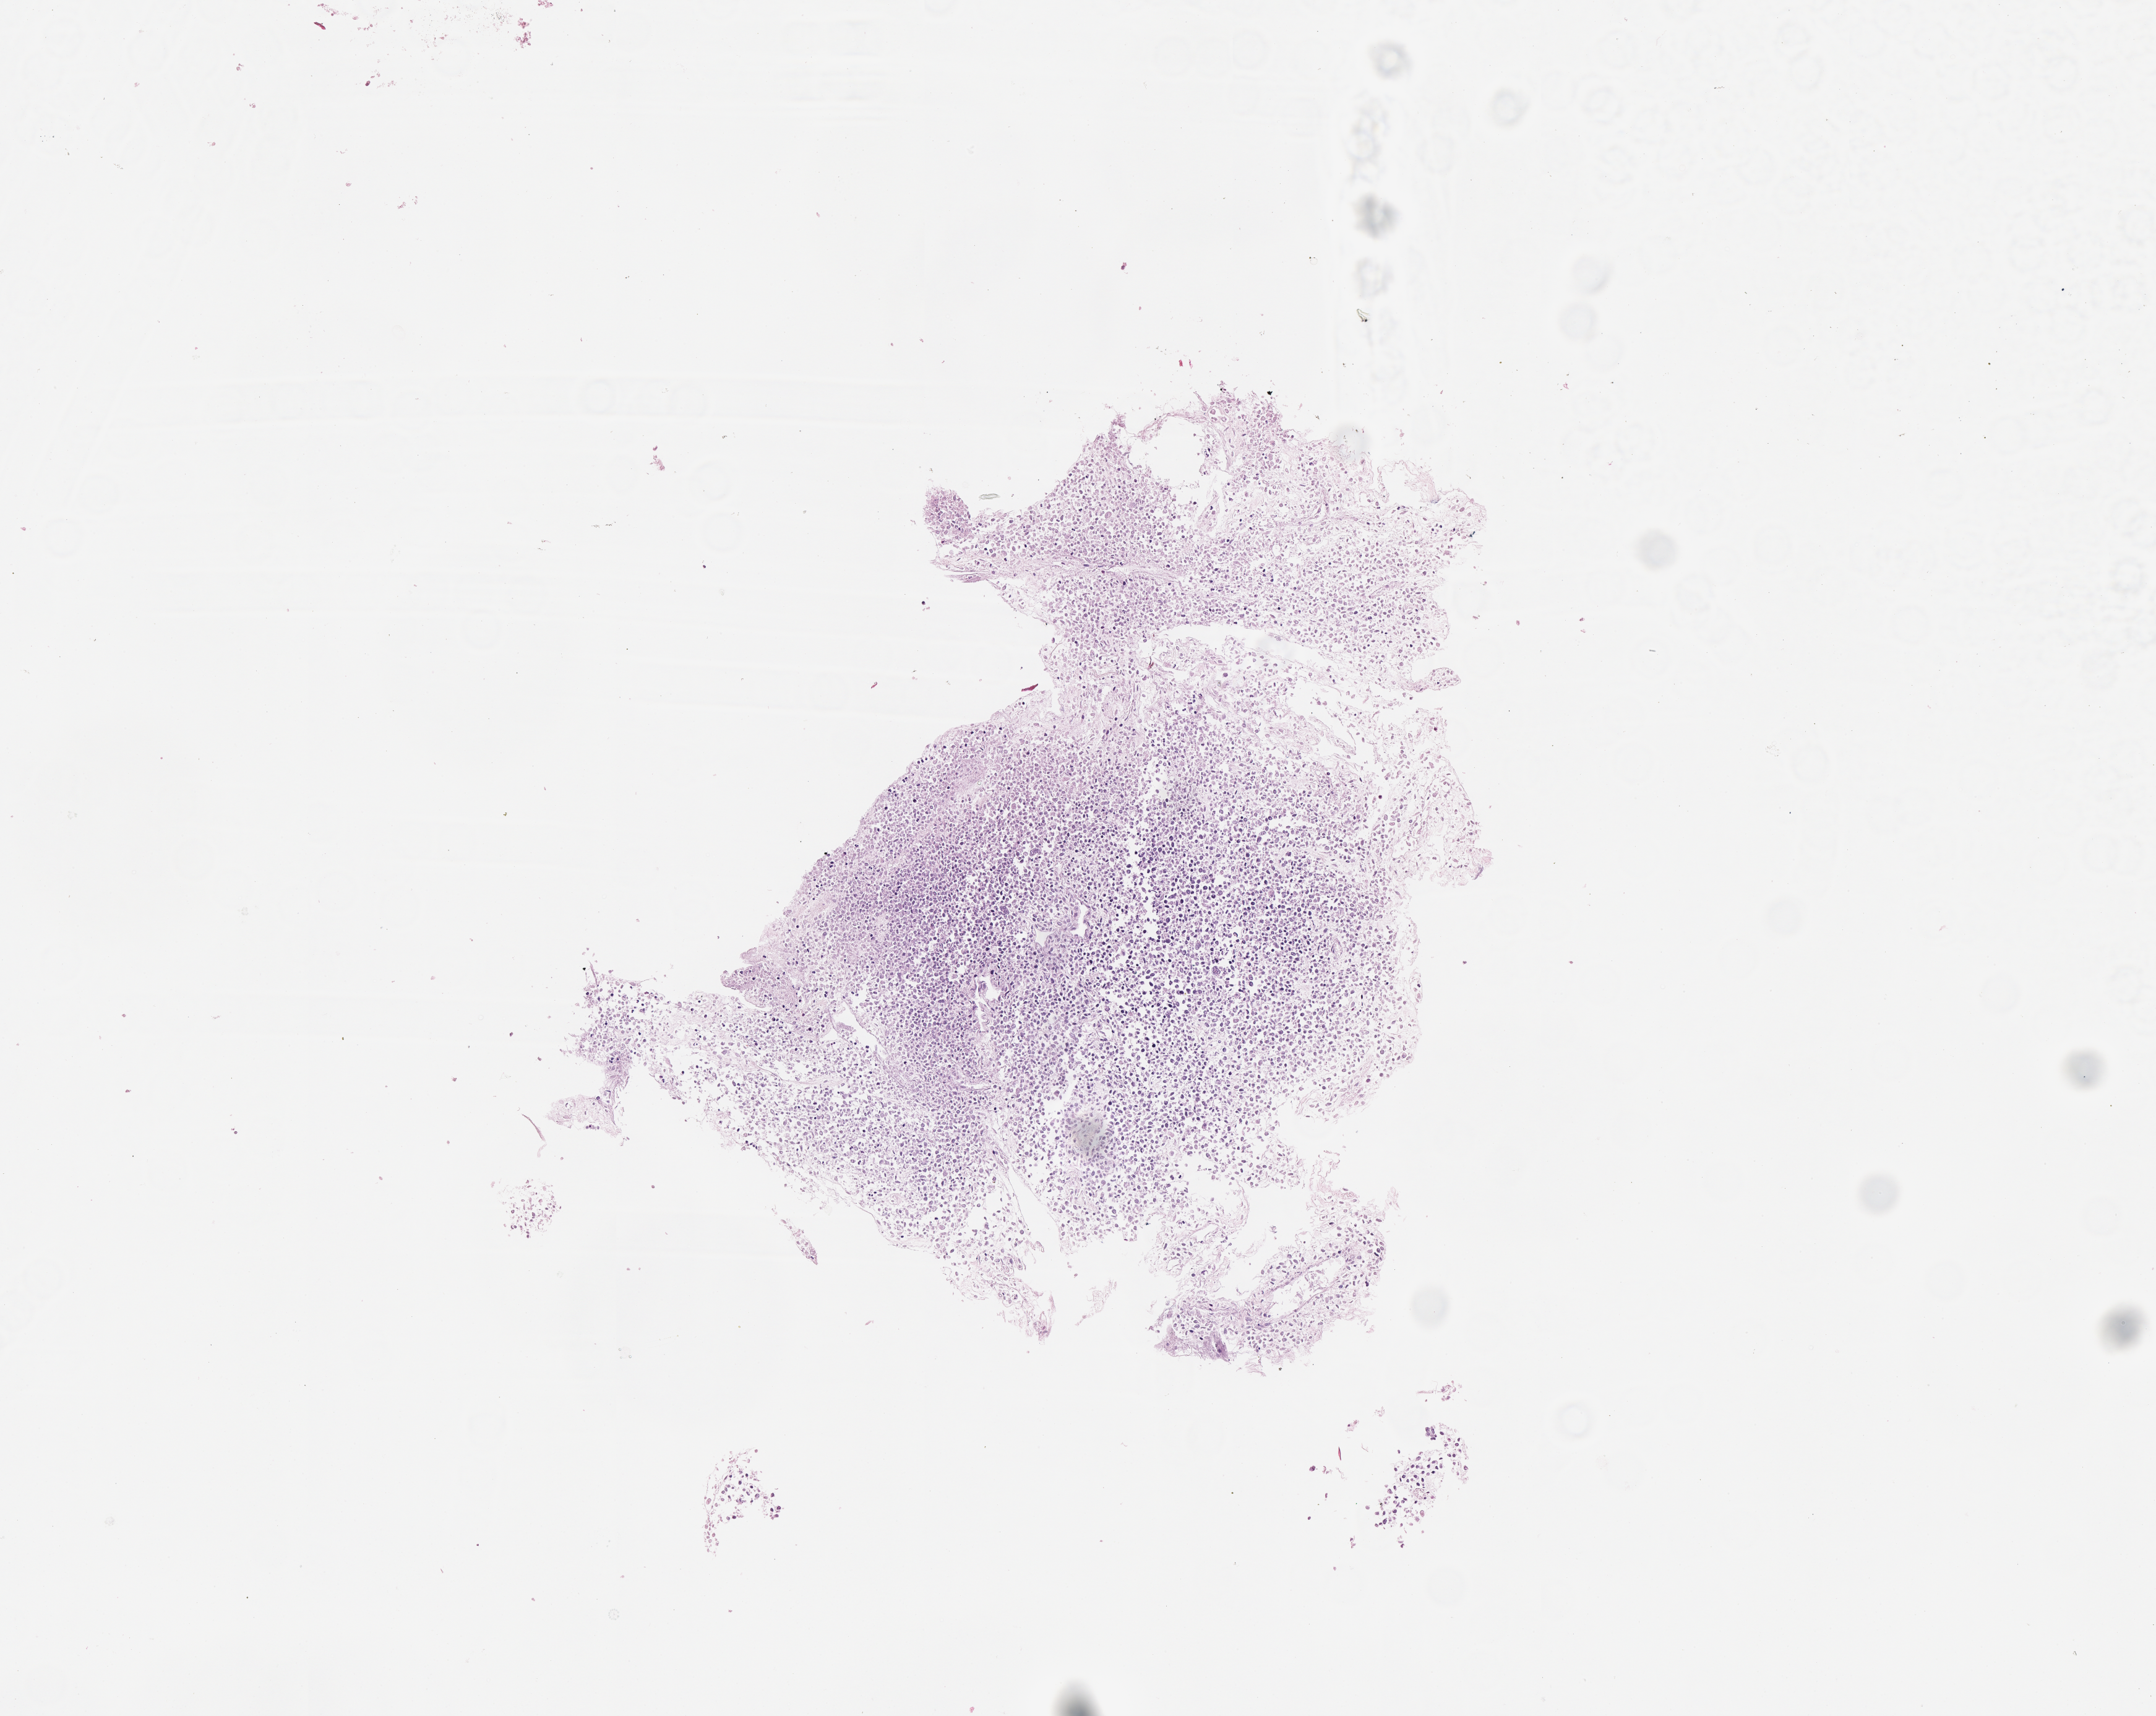
Digitized haematoxylin and eosin-stained section of tumor tissue — low-resolution overview of the scanned area, about 3.5 x 2.8 mm, formalin-fixed, paraffin-embedded (FFPE) tissue, site: bladder. Patient: male, age 18.5 years at diagnosis.
• stage (as recorded): 4
• primary site (case record): prostate
• metastatic status at presentation (as recorded): metastatic (confirmed)
• diagnosis: rhabdomyosarcoma; histological classification: embryonal rhabdomyosarcoma